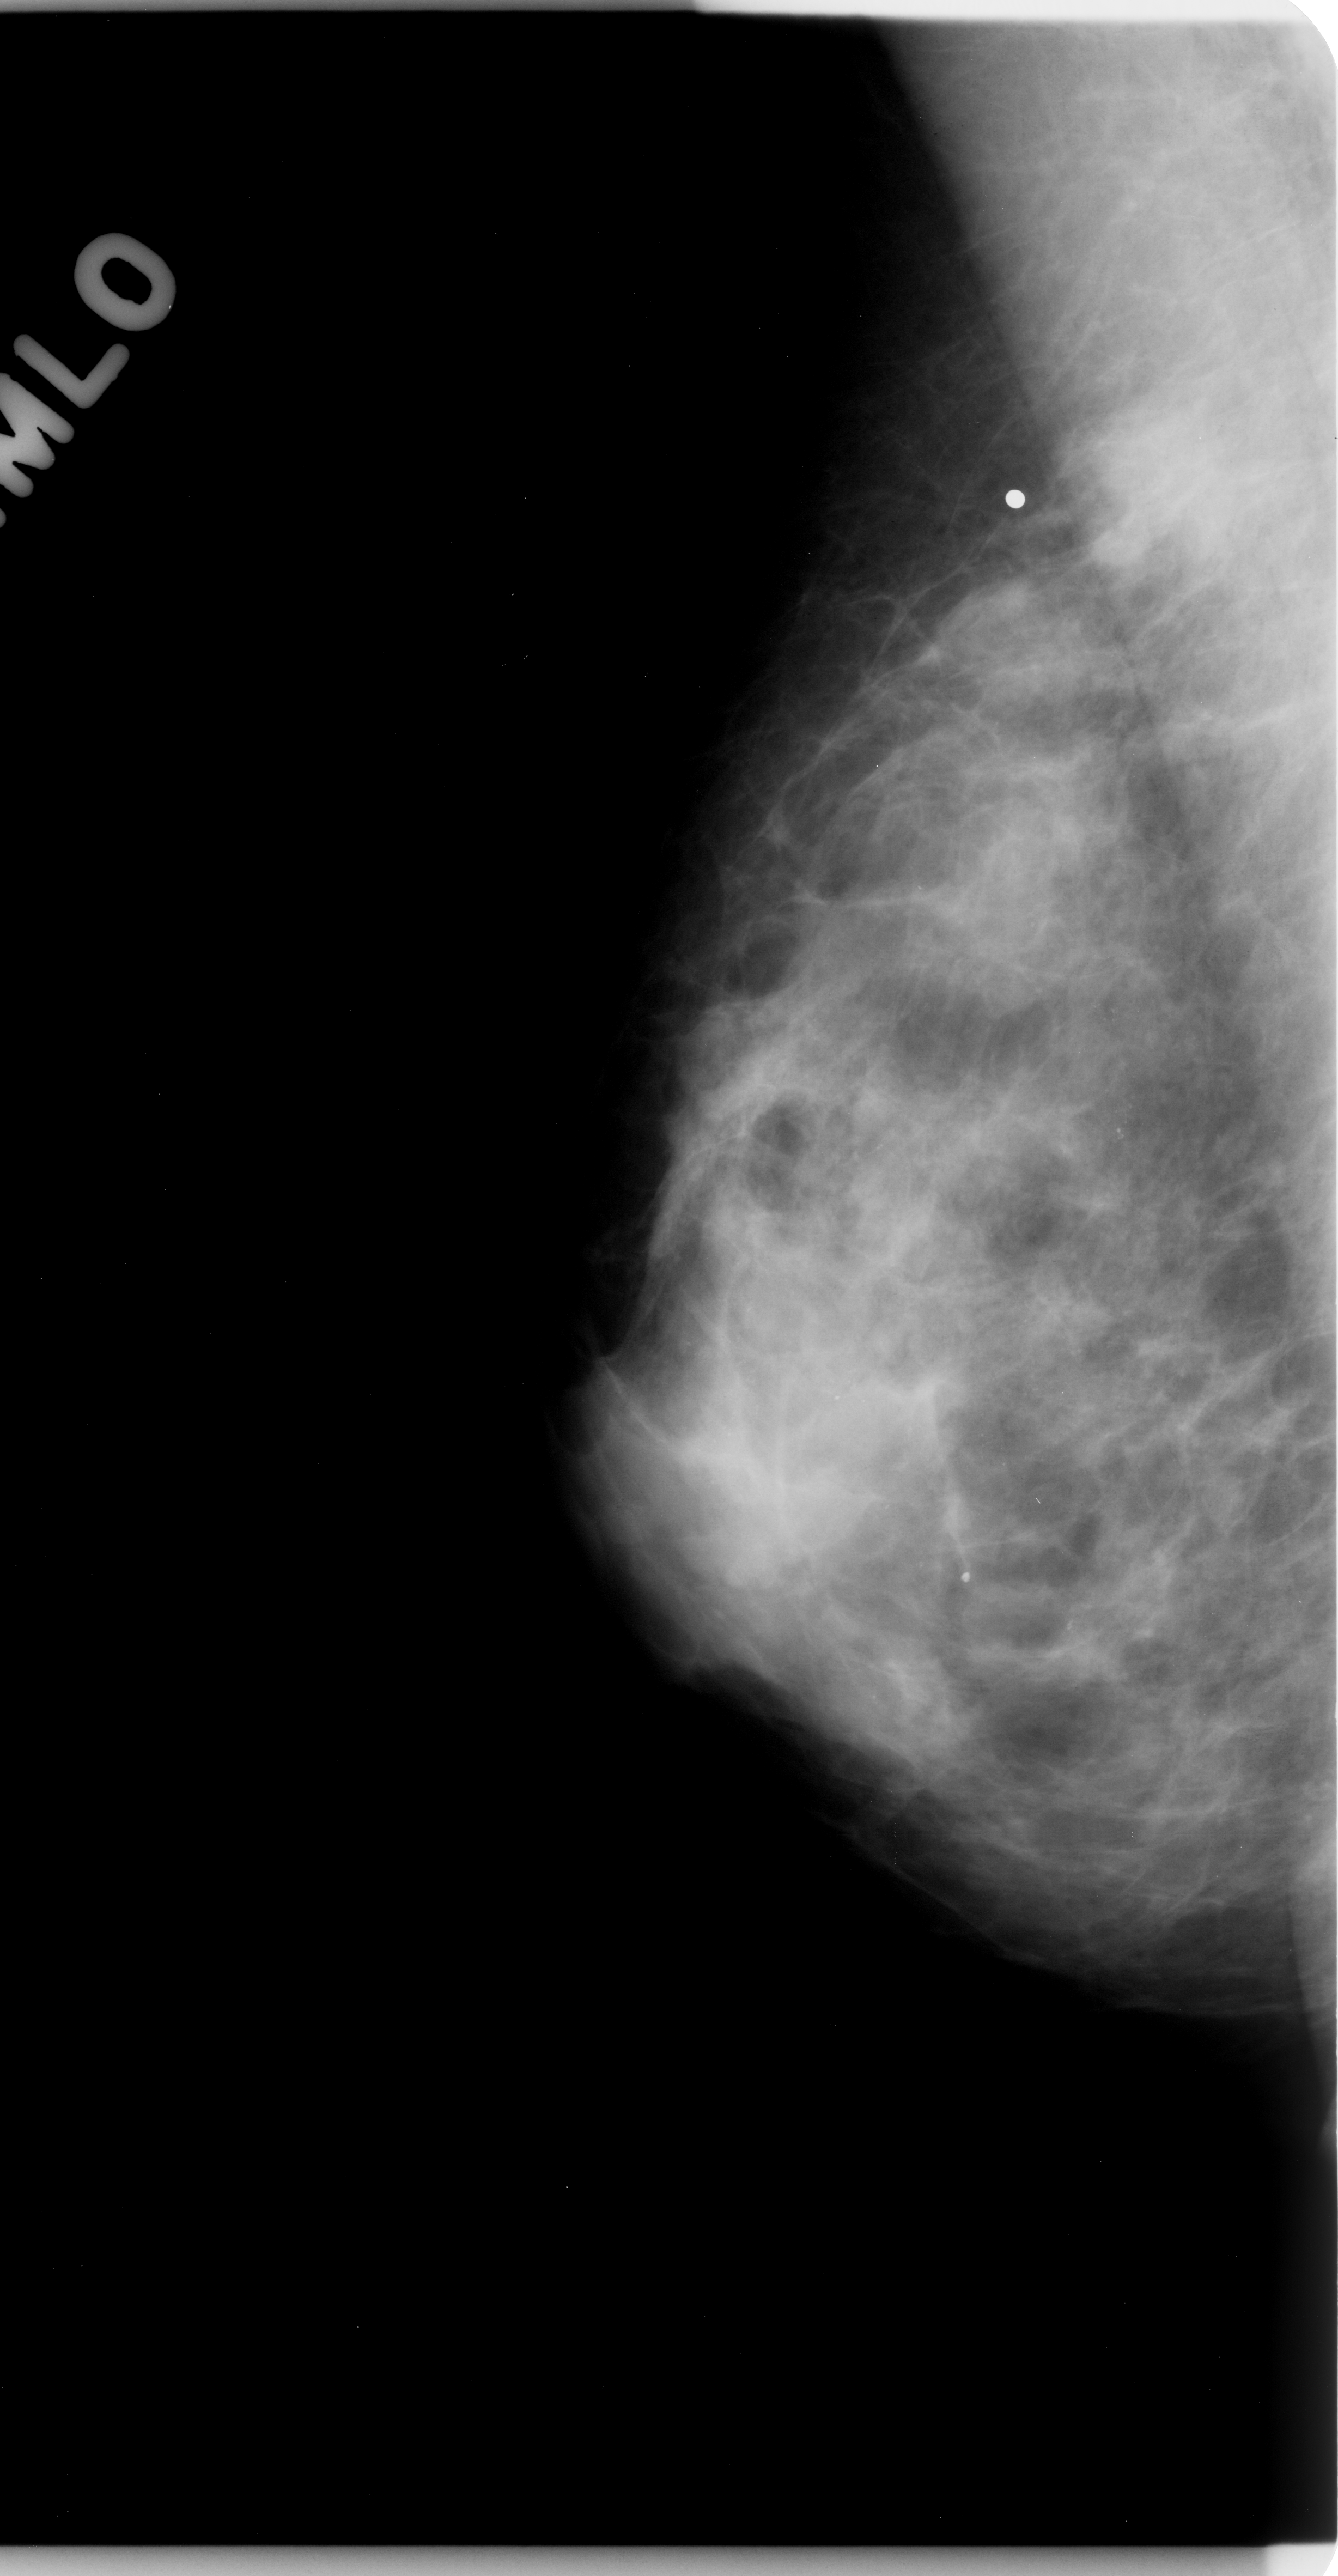
Scanned film-screen mammogram; right breast; mediolateral oblique (MLO) view; breast composition: heterogeneously dense (BI-RADS density category 3 of 4); 1338 × 2576 image matrix.
Expert-marked regions of interest on this image (one box per marked abnormality):
- mass, shape irregular, margins ill defined; BI-RADS assessment category 4; pathology result (as recorded, not read from the image): malignant: bounding box <1036,390,1218,598> (left, top, right, bottom; pixels)